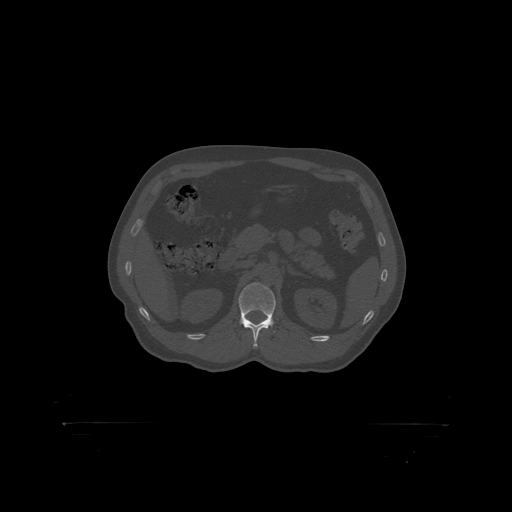
CT including the spine, one axial slice; slice 324 of 399 in the series (ordered by position); reconstruction kernel STANDARD; 120 kVp; bone window (W 1800 / L 400 HU); 512 × 512 image matrix. Male patient, age 46 years. Case-level facts recorded for this patient, not image findings: primary cancer: skin.
Structures marked on this image (semi-automatic segmentation, software-assisted and operator-edited):
- L1 vertebra: bounding box [x1, y1, x2, y2] px = [239, 282, 276, 318]